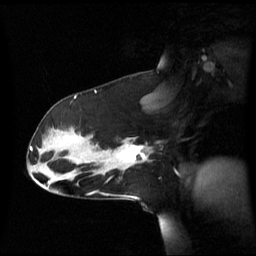
Breast MRI (dynamic contrast-enhanced), one sagittal slice; position 38 of 60 along the scan axis; dynamic contrast-enhanced series, image 2 of 3 at this slice position (ordered by acquisition); 1.5 T; TE 4.2 ms, TR 8.4 ms; 2.8 mm slice thickness; 256 × 256 image matrix, field of view 270 × 270 mm. Patient: female, 39 years. Case-level facts recorded for this patient, not image findings: setting: breast cancer imaged before/during neoadjuvant chemotherapy; receptor status: triple-negative.
Annotated regions visible in this slice (semi-automatic segmentation, software-assisted and operator-edited):
- analysis volume of interest (the breast-tissue region the enhancement analysis was run in; not a lesion): bounding box <101,138,151,173> (left, top, right, bottom; pixels)
- tumour enhancement mask (voxels above the 70 % enhancement threshold inside the analysis volume of interest): <121,145,146,162>